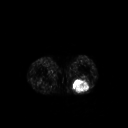
FDG PET of an extremity soft-tissue mass (from a PET/CT study), one axial slice; slice 189 of 267 in the series (ordered by position); 3.27 mm slice thickness; 128 × 128 image matrix, field of view 500 × 500 mm. Male patient, age 54 years. Case-level facts recorded for this patient, not image findings: histological type: synovial sarcoma; site of the primary tumour: left poplietal fossa.
Annotated regions visible in this slice (expert contour drawn on MRI and transferred to this co-registered scan by the dataset authors):
- gross tumour volume (mass): box from (x=72, y=78) to (x=90, y=93) px